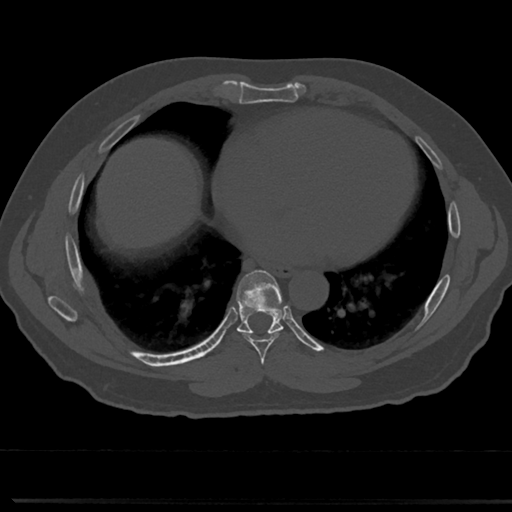
CT including the spine, one axial slice. Position 379 of 817 along the scan axis. 120 kVp. Bone window (W 1800 / L 400 HU). 0.5 mm slice thickness. 512 × 512 image matrix, field of view 355 × 355 mm. Male patient, age 61 years. Case-level facts recorded for this patient, not image findings: primary cancer: prostate.
Annotated regions visible in this slice (semi-automatic segmentation, software-assisted and operator-edited):
- T6 vertebra: box from (x=261, y=369) to (x=266, y=376) px
- T7 vertebra: (x=232, y=272)–(x=292, y=354)
- T8 vertebra: (x=242, y=328)–(x=247, y=332)